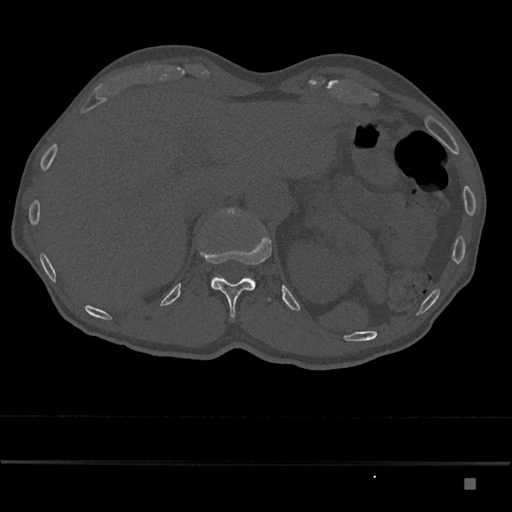
CT including the spine, one axial slice; position 600 of 797 along the scan axis; reconstruction kernel Br40s/3; 120 kVp; bone window (W 1800 / L 400 HU); 0.5 mm slice thickness; 512 × 512 image matrix, field of view 390 × 390 mm. Male patient, age 72 years. From the clinical record (not read from this slice): primary cancer: prostate.
Outlined on this slice (semi-automatically segmented with operator editing):
- L1 vertebra: bounding box <211,208,238,282> (left, top, right, bottom; pixels)
- T12 vertebra: <200,236,272,318>